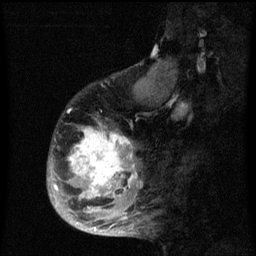
Breast MRI (dynamic contrast-enhanced), one sagittal slice. Position 21 of 60 along the scan axis. Dynamic contrast-enhanced series, image 2 of 3 at this slice position (ordered by acquisition). 1.5 T. TE 4.2 ms, TR 8 ms. 2 mm slice thickness. 256 × 256 image matrix. Female patient, age 50 years.
Annotated regions visible in this slice (semi-automatic segmentation, software-assisted and operator-edited):
- analysis volume of interest (the breast-tissue region the enhancement analysis was run in; not a lesion): bounding box [x1, y1, x2, y2] px = [47, 90, 142, 216]
- tumour enhancement mask (voxels above the 70 % enhancement threshold inside the analysis volume of interest): [54, 127, 138, 213]